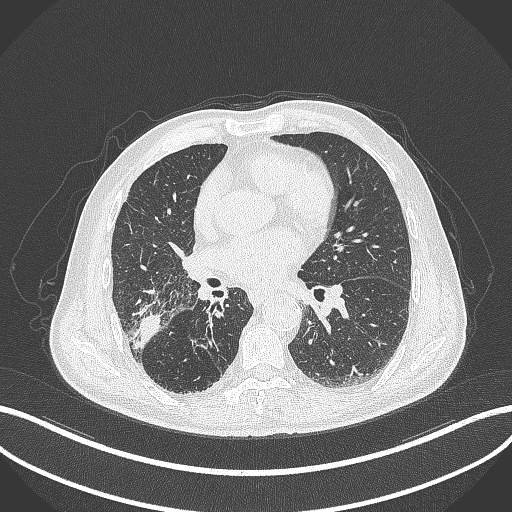
Chest CT, one axial slice. Slice 204 of 429 in the series (ordered by position). 120 kVp. Lung window (W 1500 / L -600 HU). 1 mm slice thickness. 512 × 512 image matrix, field of view 400 × 400 mm. Patient: male, 72 years. Case-level facts recorded for this patient, not image findings: clinical TNM (as recorded): T3 N2 M0.
Structures marked on this image (bounding box drawn by a radiologist):
- lung tumour (recorded histology: adenocarcinoma): bounding box <127,309,164,353> (left, top, right, bottom; pixels)